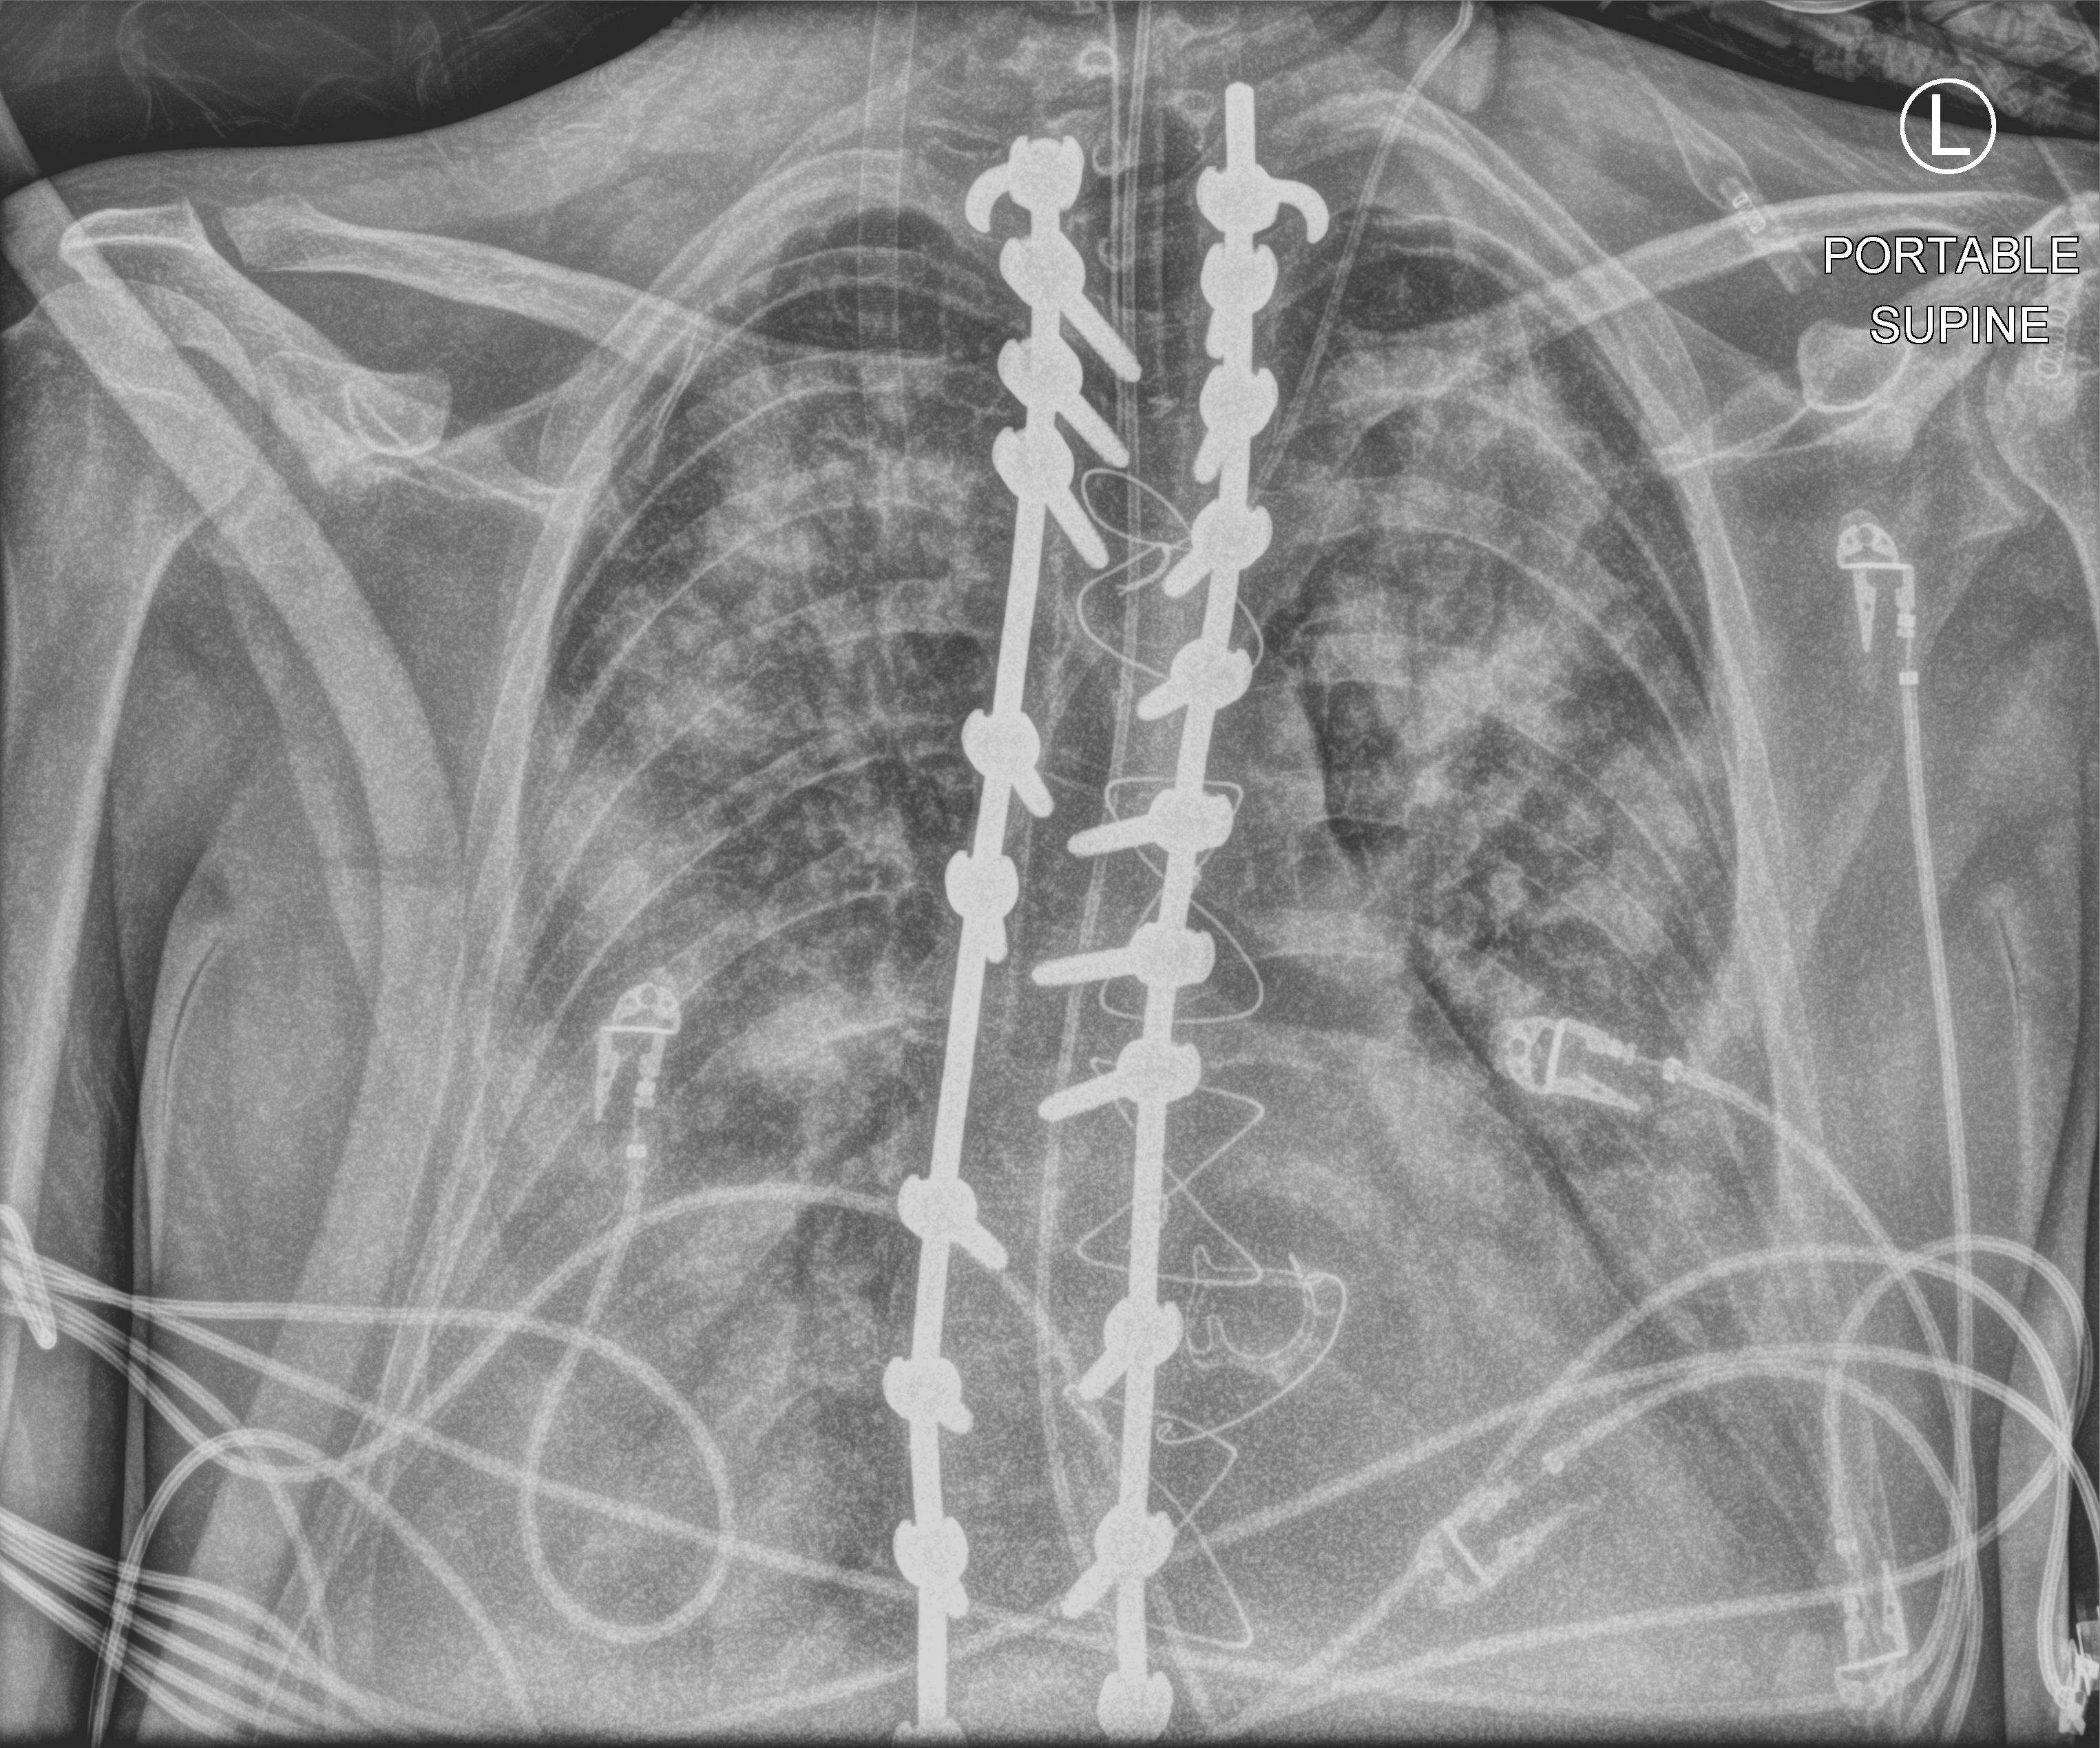
Bedside chest radiograph (computed radiography); anteroposterior (AP) projection. Adult patient hospitalised with COVID-19, age 18–59 years.
Hospital-stay facts (about this admission, not read from this image; timing relative to this image not recorded): hypertension (admission record): no; mechanically ventilated during this hospital stay: yes.